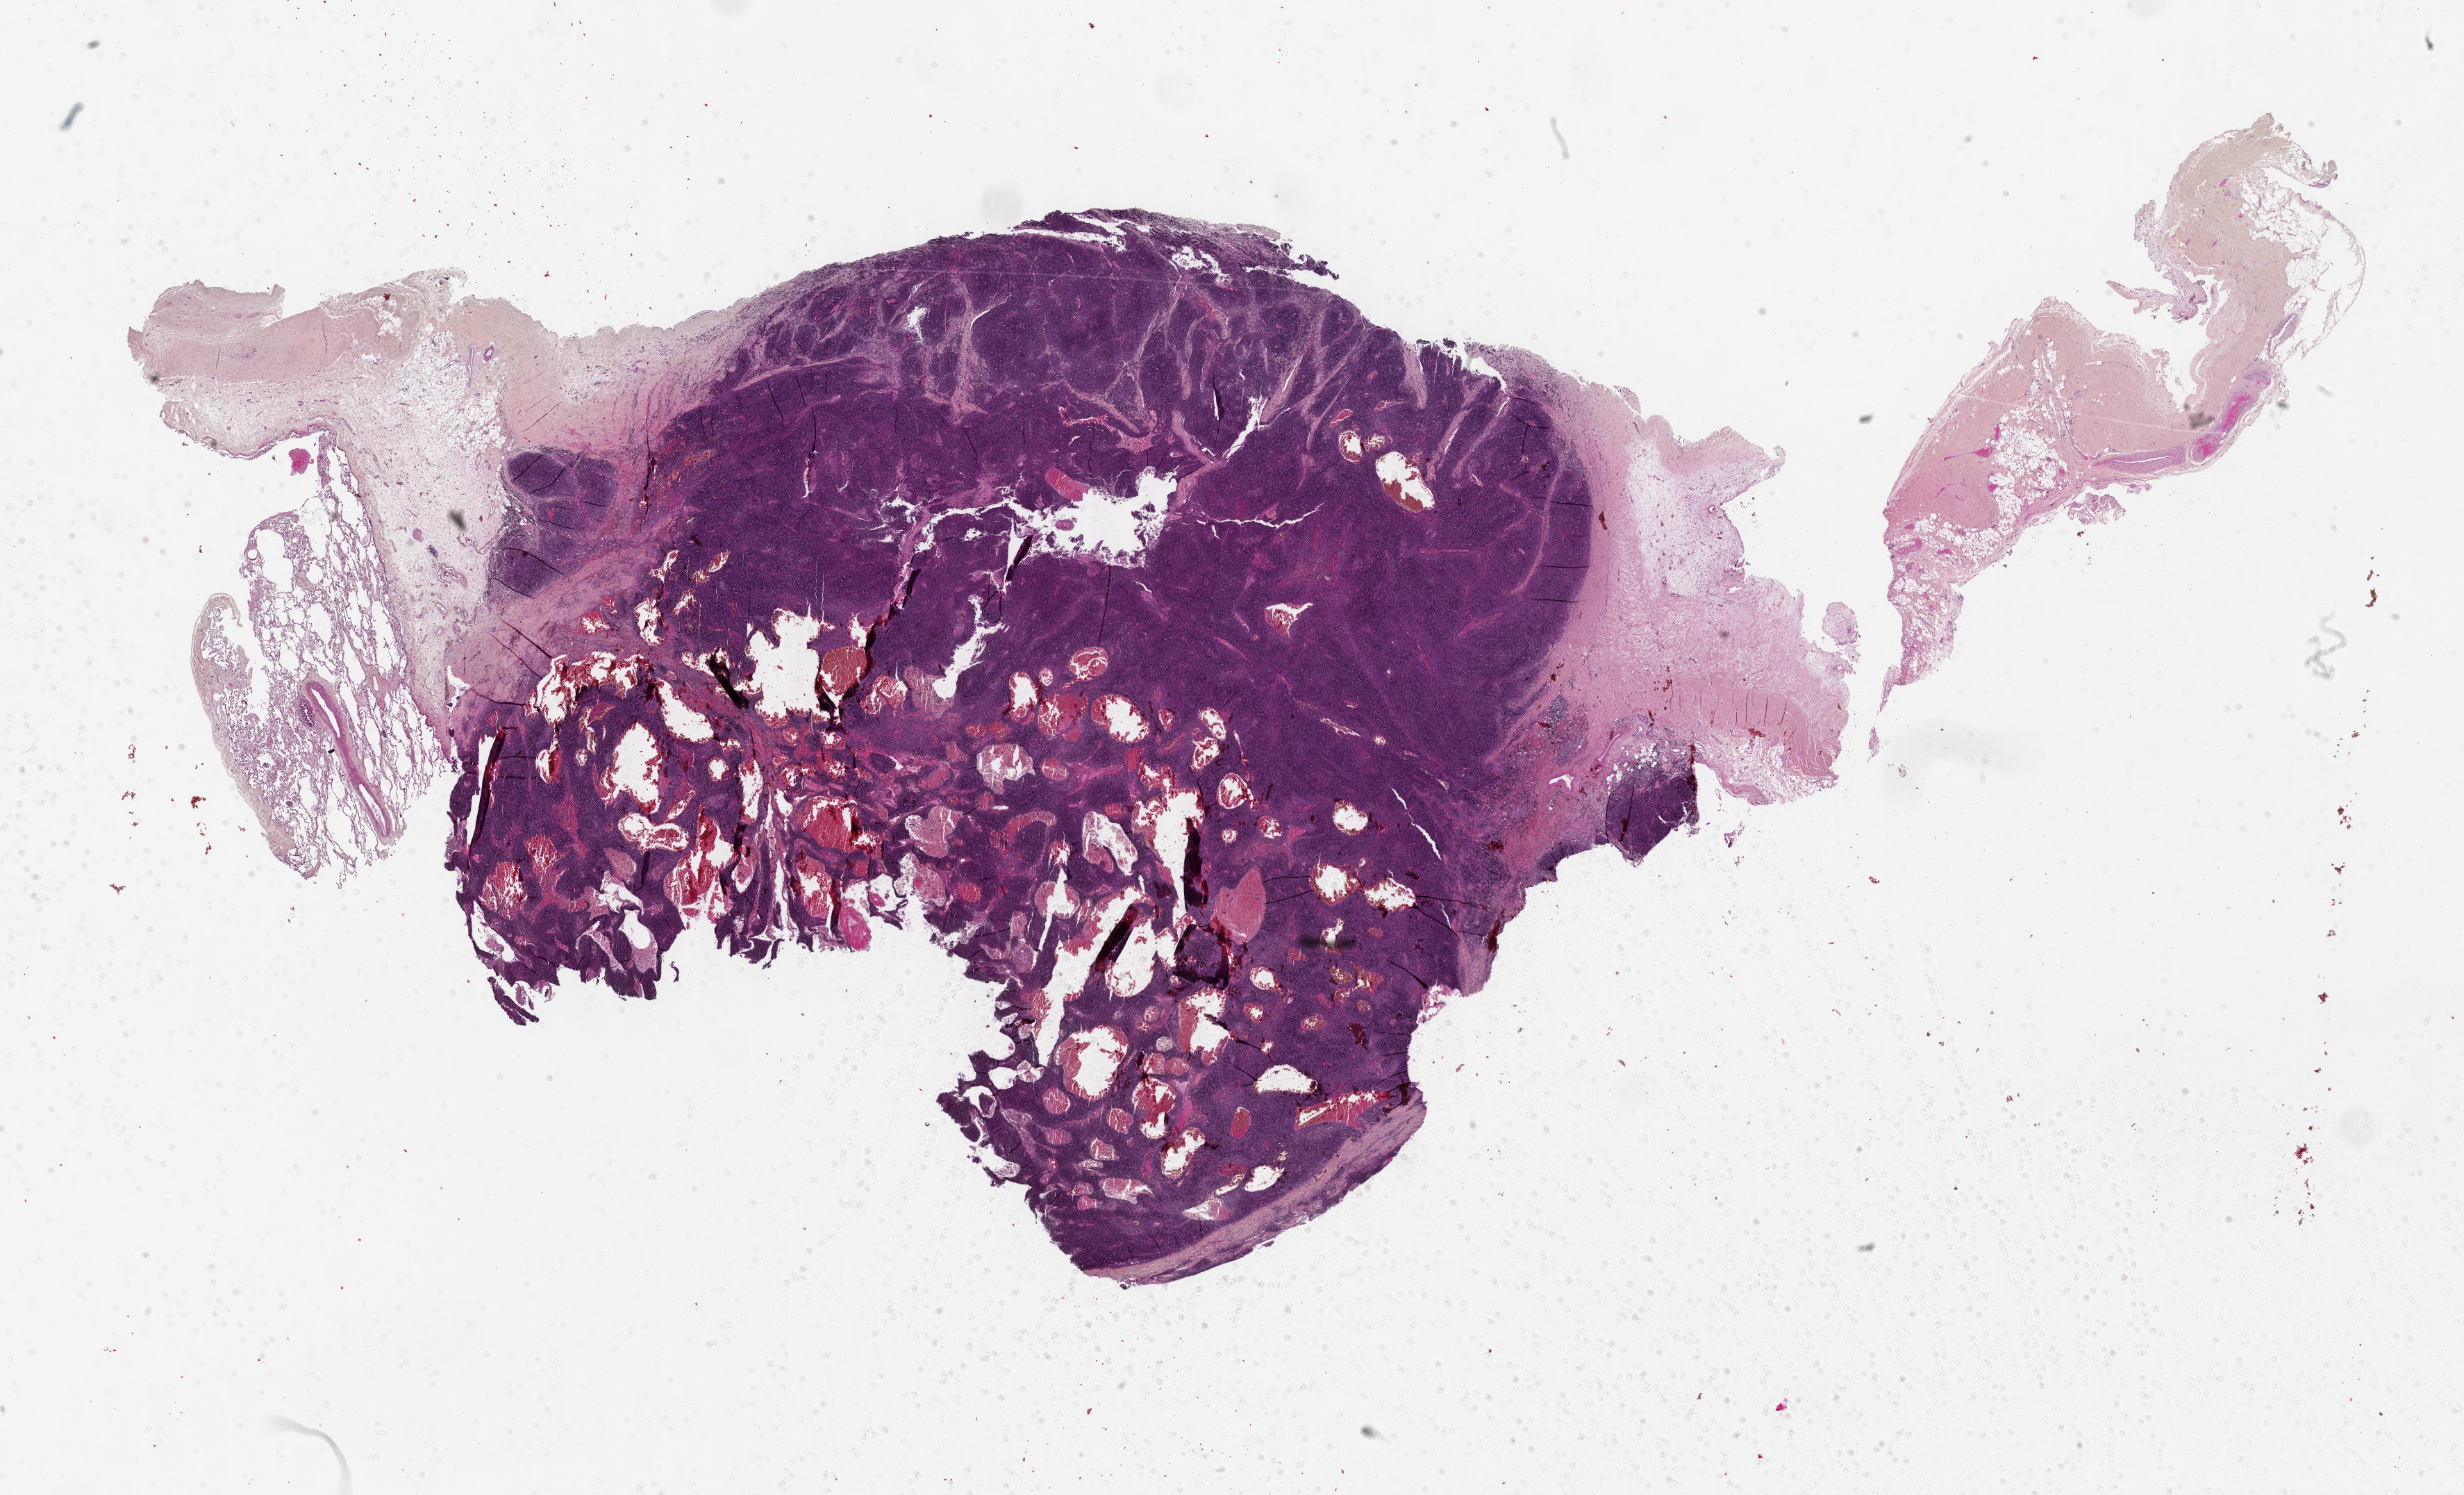
Digitized H&E-stained tissue section (whole slide), a low-resolution overview of the entire scanned area, about 28.7 x 17.4 mm, formalin-fixed paraffin-embedded (FFPE) diagnostic section, sample: primary tumour, thymus. Patient: female, age at initial diagnosis 65 years.
- diagnosis: Thymoma, type B3, malignant